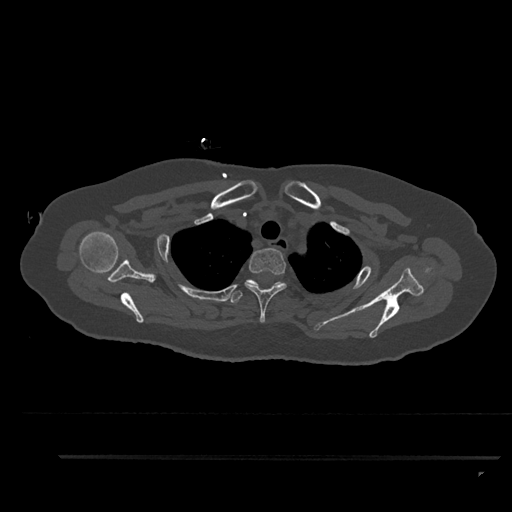
CT including the spine, one axial slice; slice 712 of 797 in the series (ordered by position); reconstruction kernel Br40s/3; bone window (W 1800 / L 400 HU); 0.5 mm slice thickness; 512 × 512 image matrix. Patient: female, 44 years. Case-level facts recorded for this patient, not image findings: primary cancer: renal; vertebrae with lytic lesions (as recorded): L1.
Outlined on this slice (semi-automatically segmented with operator editing):
- T1 vertebra: bounding box [x1, y1, x2, y2] px = [271, 282, 285, 288]
- T2 vertebra: [245, 248, 287, 323]
- T3 vertebra: [229, 279, 283, 303]